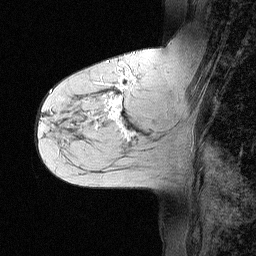
Breast MRI (dynamic contrast-enhanced), one sagittal slice; position 25 of 64 along the scan axis; dynamic contrast-enhanced study with each time point stored as its own series, time point 2 of 3 at this slice position (early post-contrast, ordered by acquisition time); 1.5 T; TE 4.5 ms, TR 11 ms; 2.06 mm slice thickness; 256 × 256 image matrix, field of view 200 × 200 mm. Female patient, age 55 years. Case-level facts recorded for this patient, not image findings: setting: breast cancer imaged before/during neoadjuvant chemotherapy; receptor status: triple-negative.
Annotated regions visible in this slice (semi-automatically segmented with operator editing):
- analysis volume of interest (the breast-tissue region the enhancement analysis was run in; not a lesion): bounding box [x1, y1, x2, y2] px = [71, 63, 147, 145]
- tumour enhancement mask (voxels above the 90 % enhancement threshold inside the analysis volume of interest): [98, 74, 135, 136]